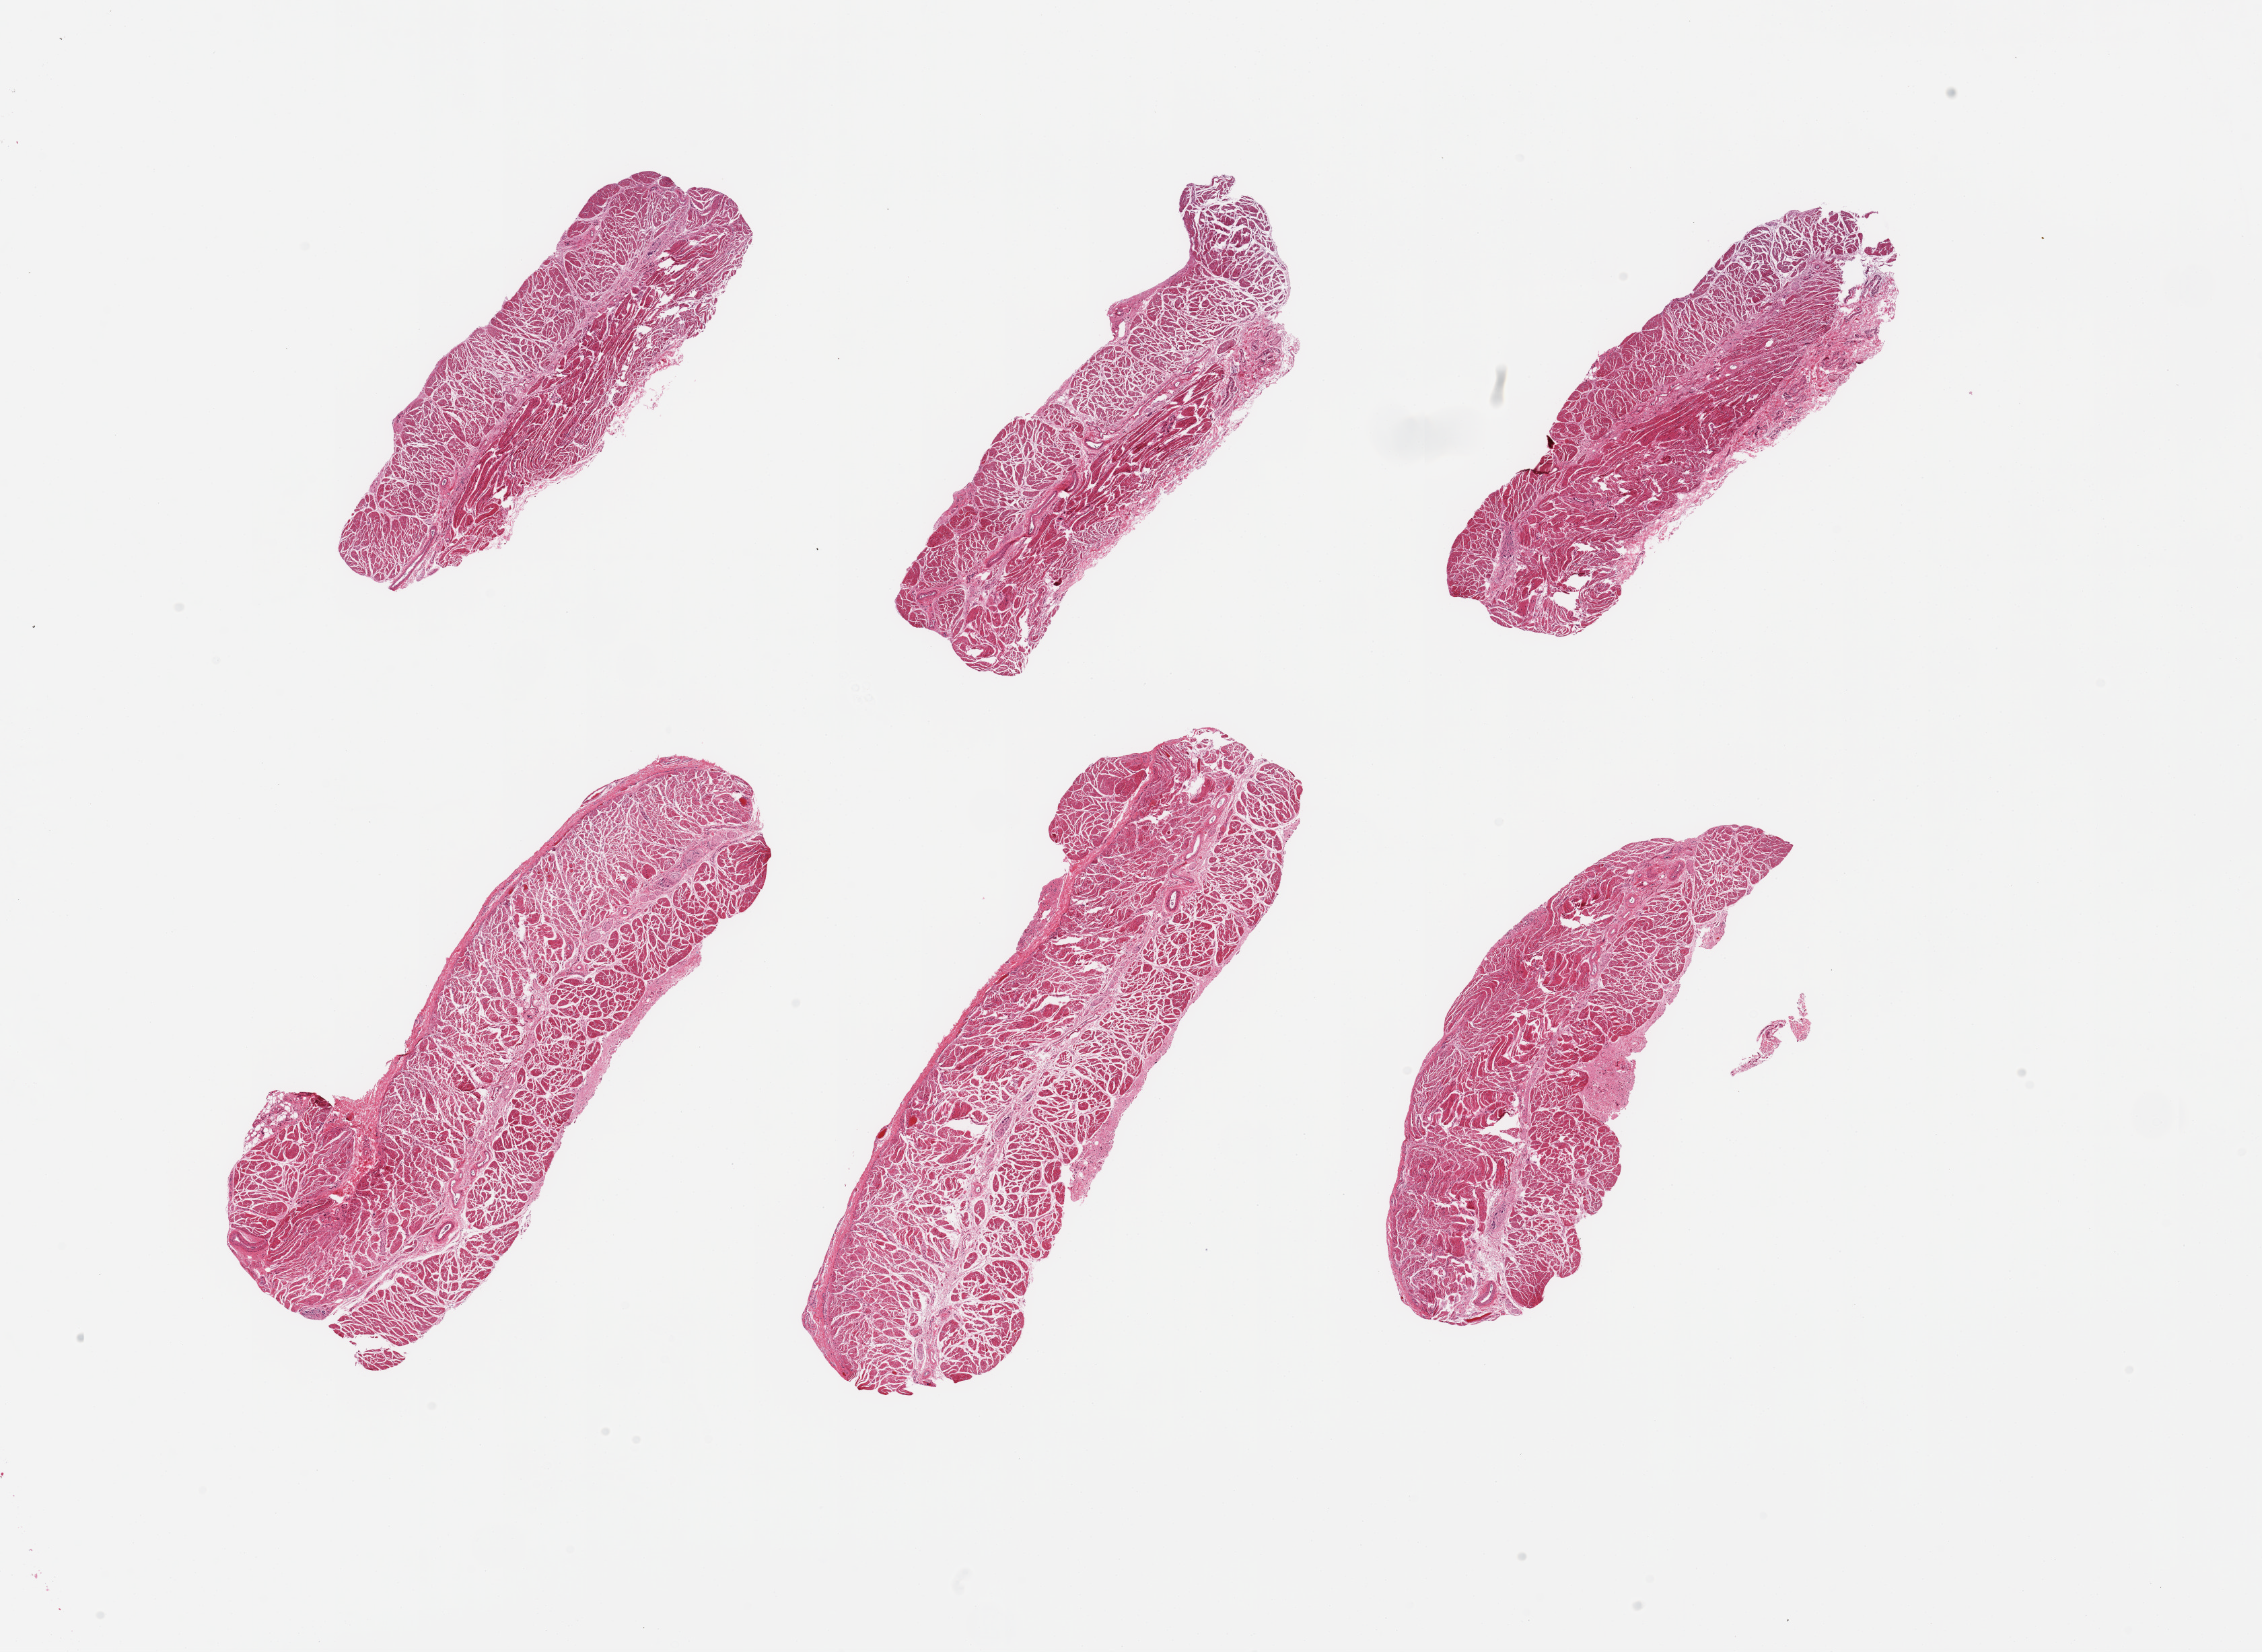
H&E whole-slide image, brightfield — a low-resolution overview of the entire scanned area, about 26.6 x 19.4 mm (from a 20x scan), PAXgene-fixed, paraffin-embedded tissue, sampled site (target tissue): gastroesophageal junction, tissue donor sample. Male donor.
Reviewer comment on this tissue sample: 6 pieces, confirmed target muscularis.